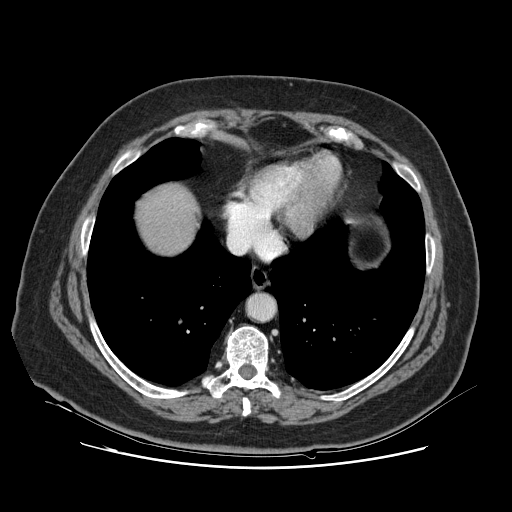
Contrast-enhanced abdominal CT, one axial slice. Position 118 of 132 along the scan axis. Intravenous contrast given. Soft-tissue window (W 400 / L 40 HU). 2.5 mm slice thickness. 512 × 512 image matrix, field of view 391 × 391 mm. Female patient, age 73 years. From the clinical record (not read from this slice): diagnosis: colorectal cancer liver metastases, imaged before liver resection; multiple liver metastases: no; largest metastasis: 7 cm.
Structures marked on this image (manually delineated by an expert):
- liver: box from (x=136, y=187) to (x=195, y=255) px
- planned liver remnant (the part of the liver to remain after resection): (x=137, y=187)–(x=195, y=255)